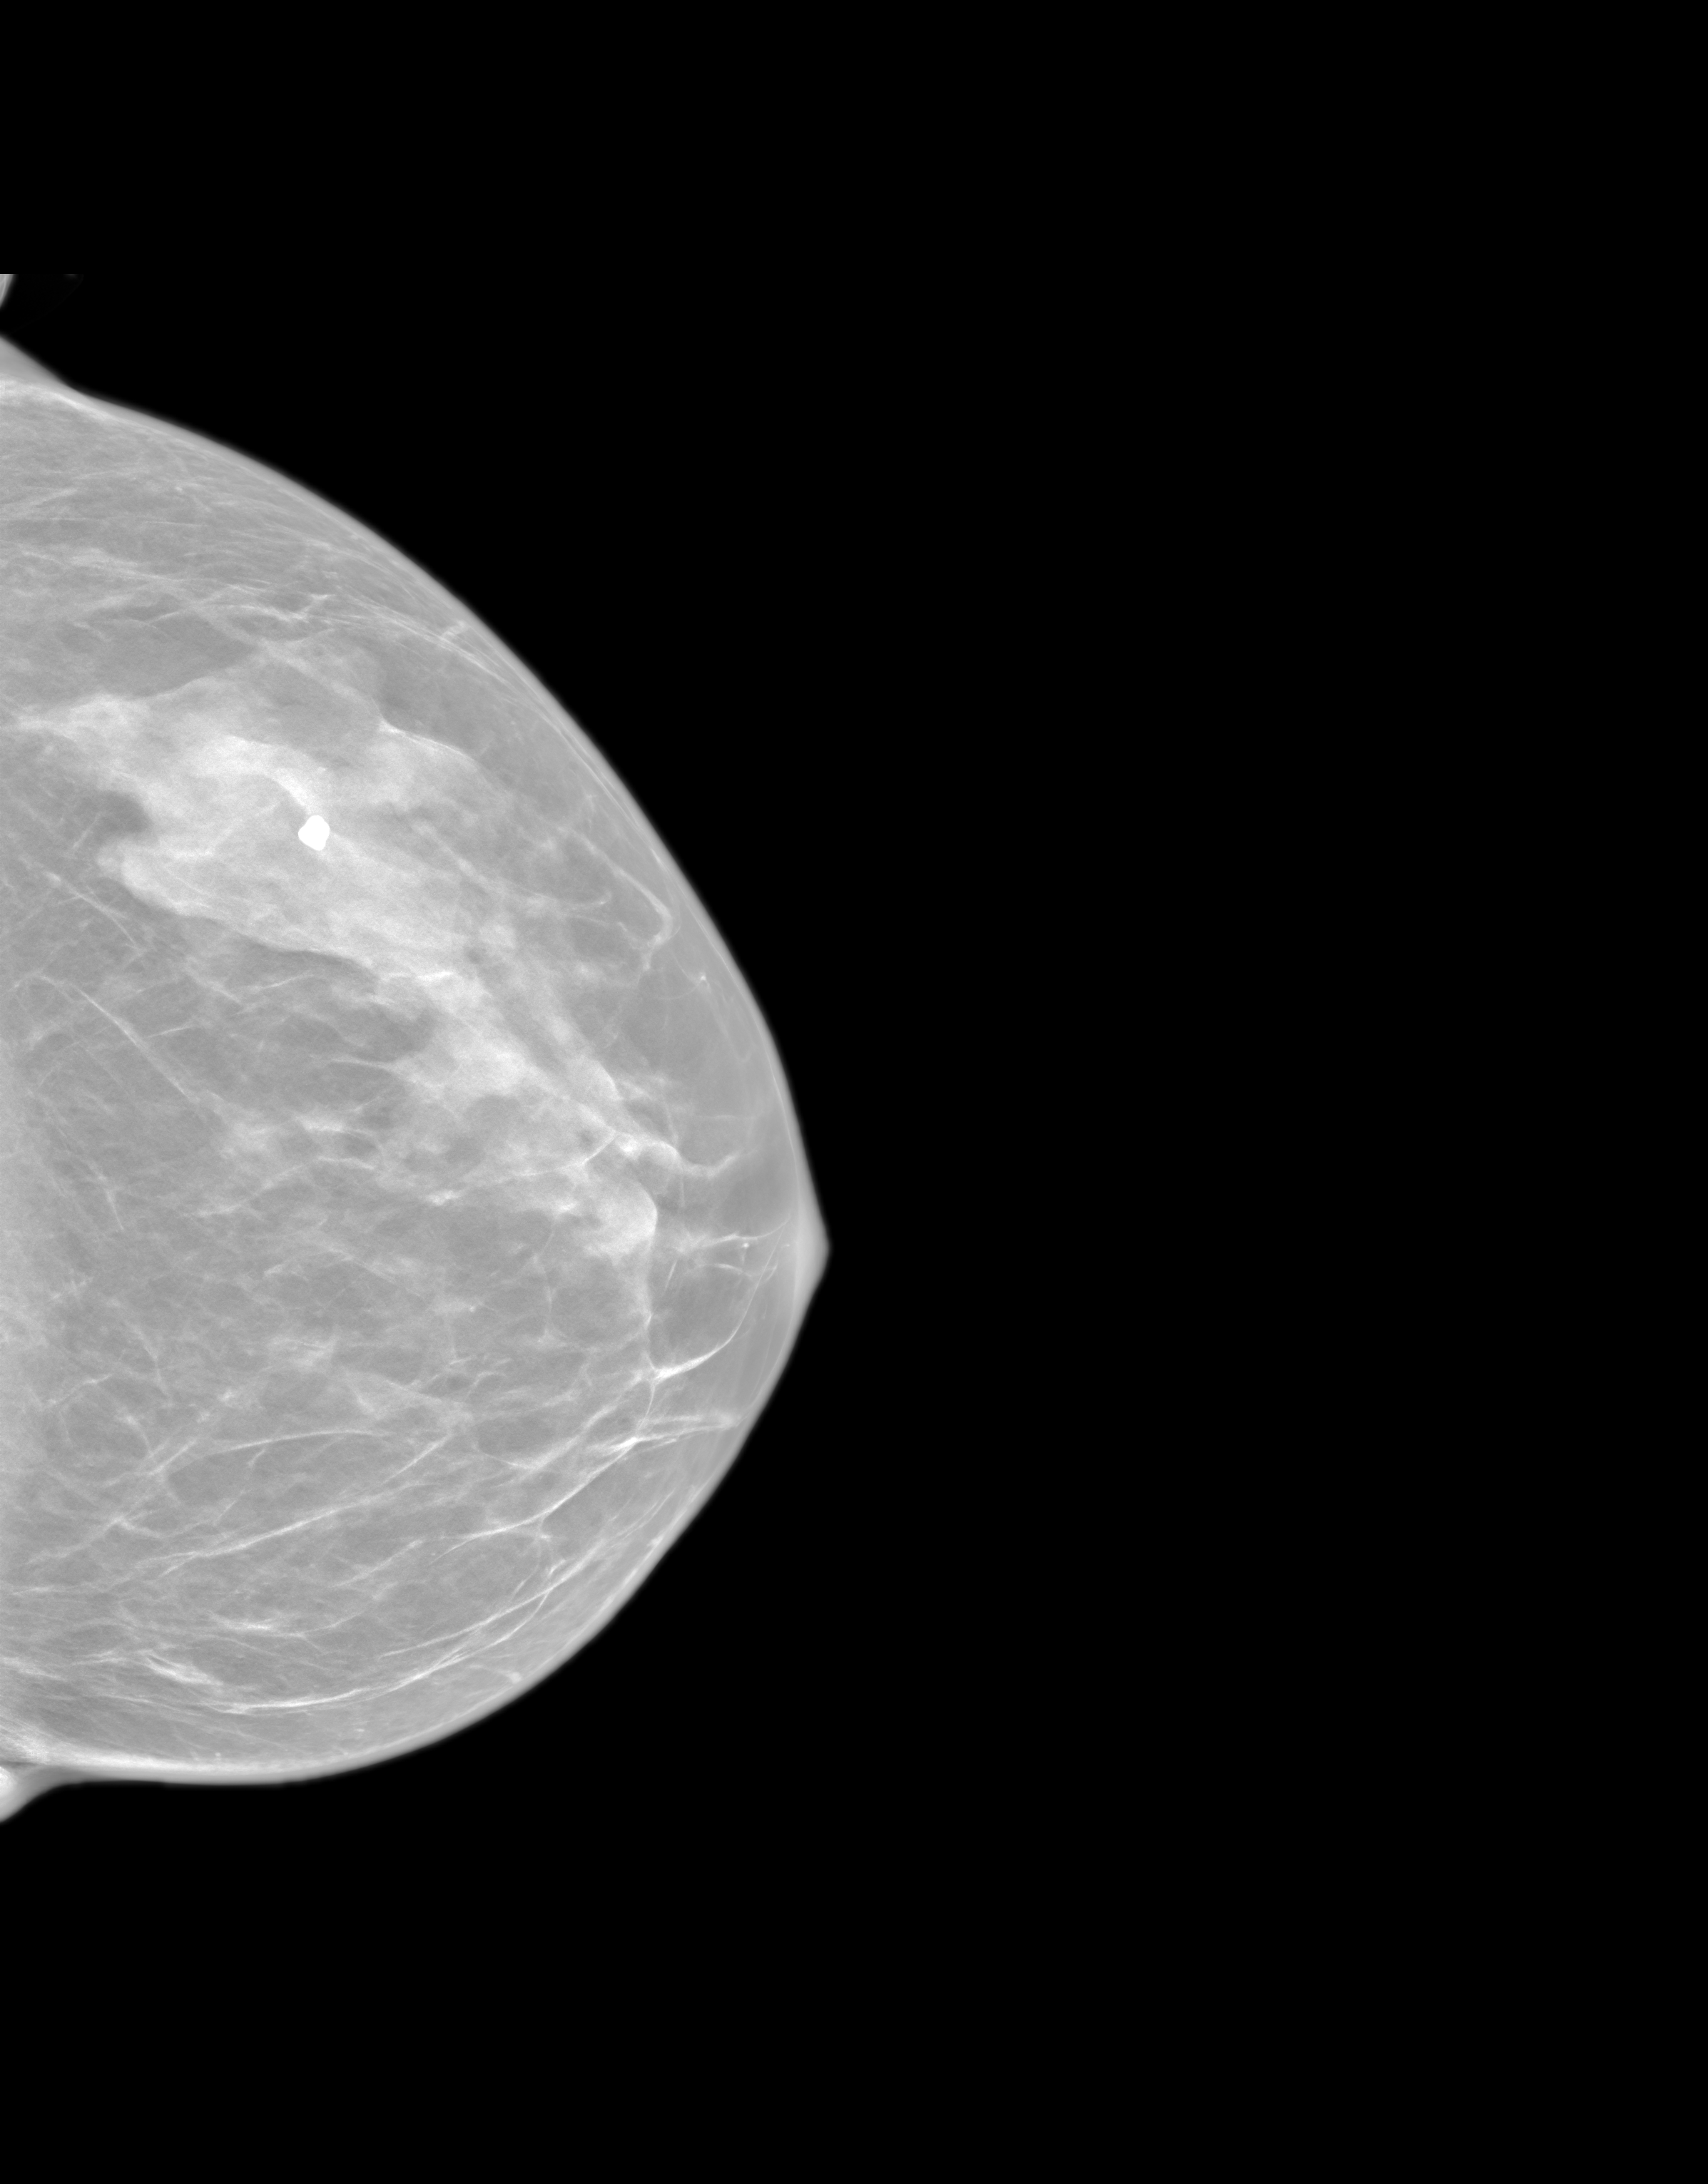
Synthetic 2-D view generated from a tomosynthesis acquisition (not an FFDM exposure); left breast; cranio-caudal projection; screening examination; system: SenoIris_1SP1.2(425). Patient: female, 51 years.
Final BI-RADS category for the screening round (tomosynthesis exam, both breasts): category 2.